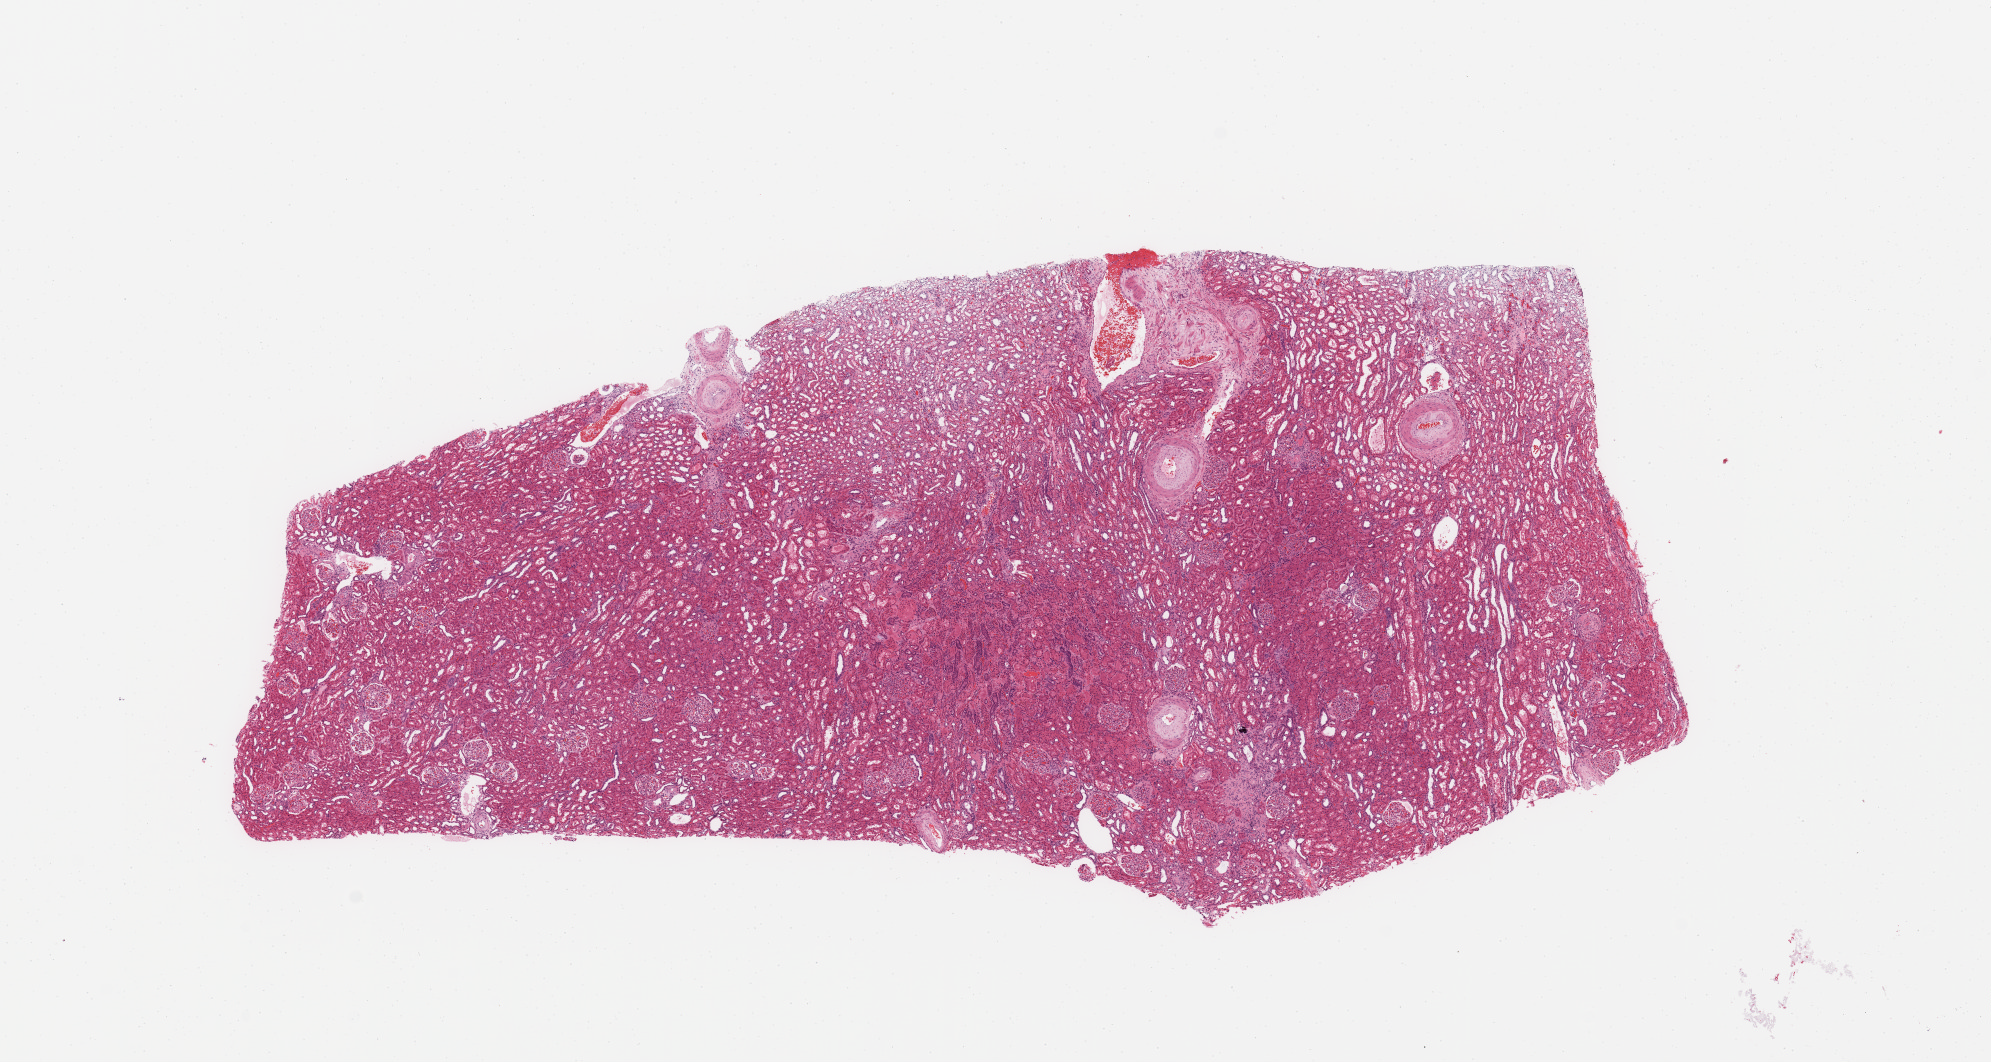
H&E-stained whole-slide image, low-resolution overview of the scanned area, about 15.8 x 8.4 mm (acquisition: 20x scan). Normal (non-tumour) tissue sample, sampled site: kidney. Patient: female, age 56 years.
* this section: normal (non-tumour) tissue from the same patient
* patient diagnosis: Renal cell carcinoma, NOS